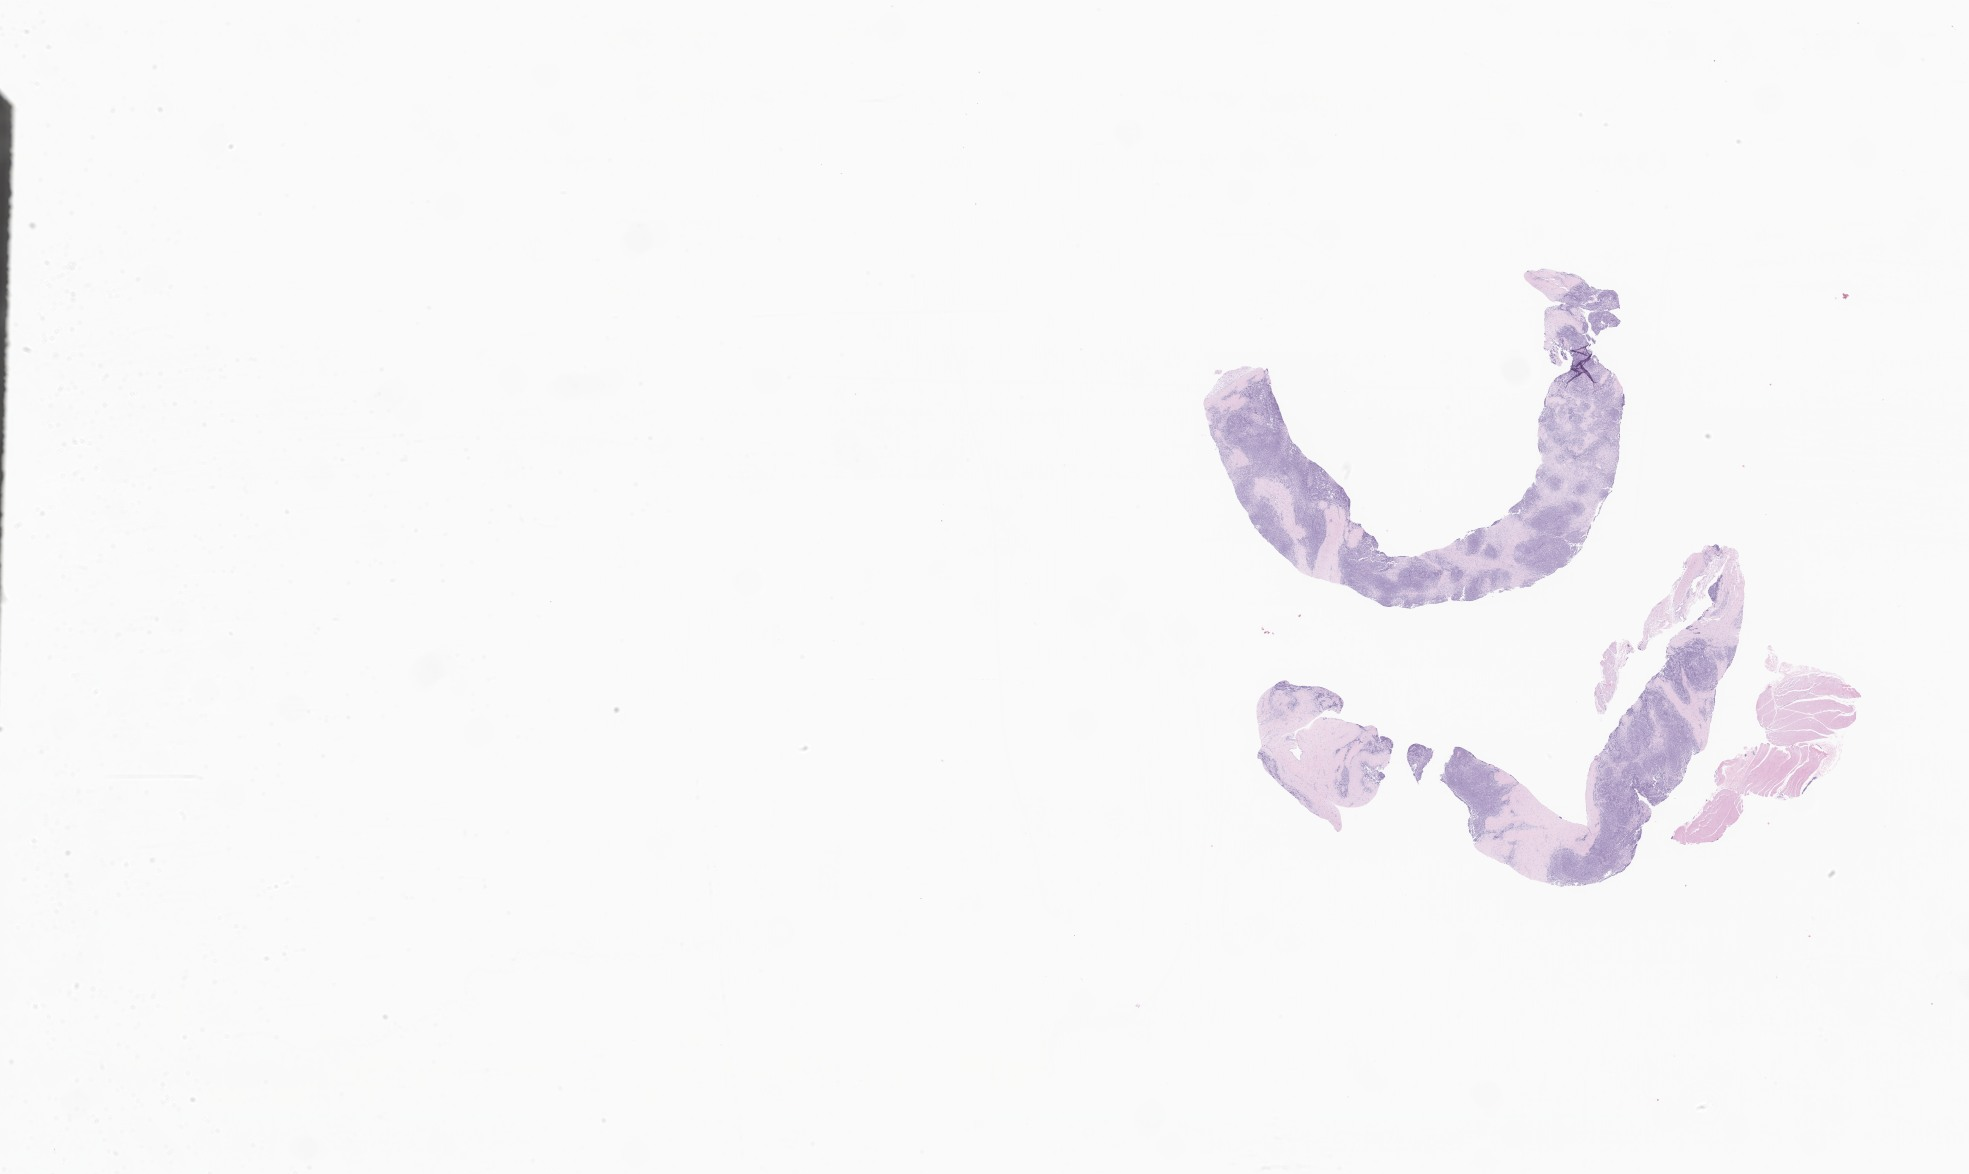
Haematoxylin and eosin whole-slide image of tumor tissue from the lower limb — whole scanned area (about 33.2 x 19.8 mm) shown as a low-resolution overview, formalin-fixed paraffin-embedded section. Female patient, age 136 months (11 years 4 months).
Diagnosis: Alveolar rhabdomyosarcoma.